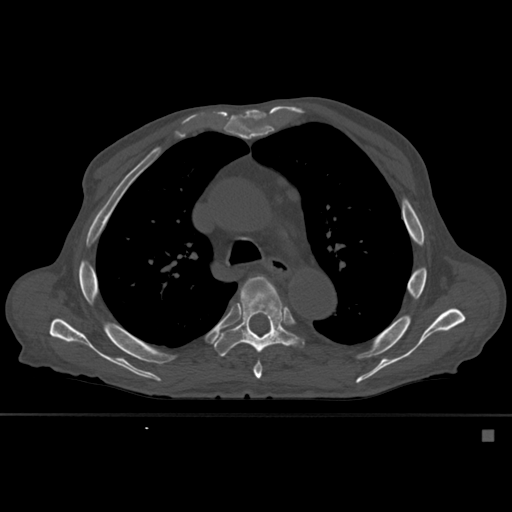
CT including the spine, one axial slice; position 389 of 527 along the scan axis; bone window (W 1800 / L 400 HU); 1.5 mm slice thickness; 512 × 512 image matrix. Patient: male, 78 years. From the clinical record (not read from this slice): primary cancer: prostate.
Outlined on this slice (semi-automatic segmentation, software-assisted and operator-edited):
- T5 vertebra: bounding box <249,277,276,379> (left, top, right, bottom; pixels)
- T6 vertebra: <214,276,299,356>